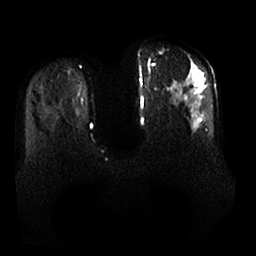
Breast MRI, one axial slice; slice 11 of 25 in the series (ordered by position); diffusion-weighted series; image 2 of 4 stored at this slice position (different b-values; order by instance number); 1.5 T; 4 mm slice thickness; 256 × 256 image matrix. Female patient.
Structures marked on this image (expert manual segmentation):
- tumour on diffusion-weighted imaging: box from (x=192, y=73) to (x=195, y=84) px